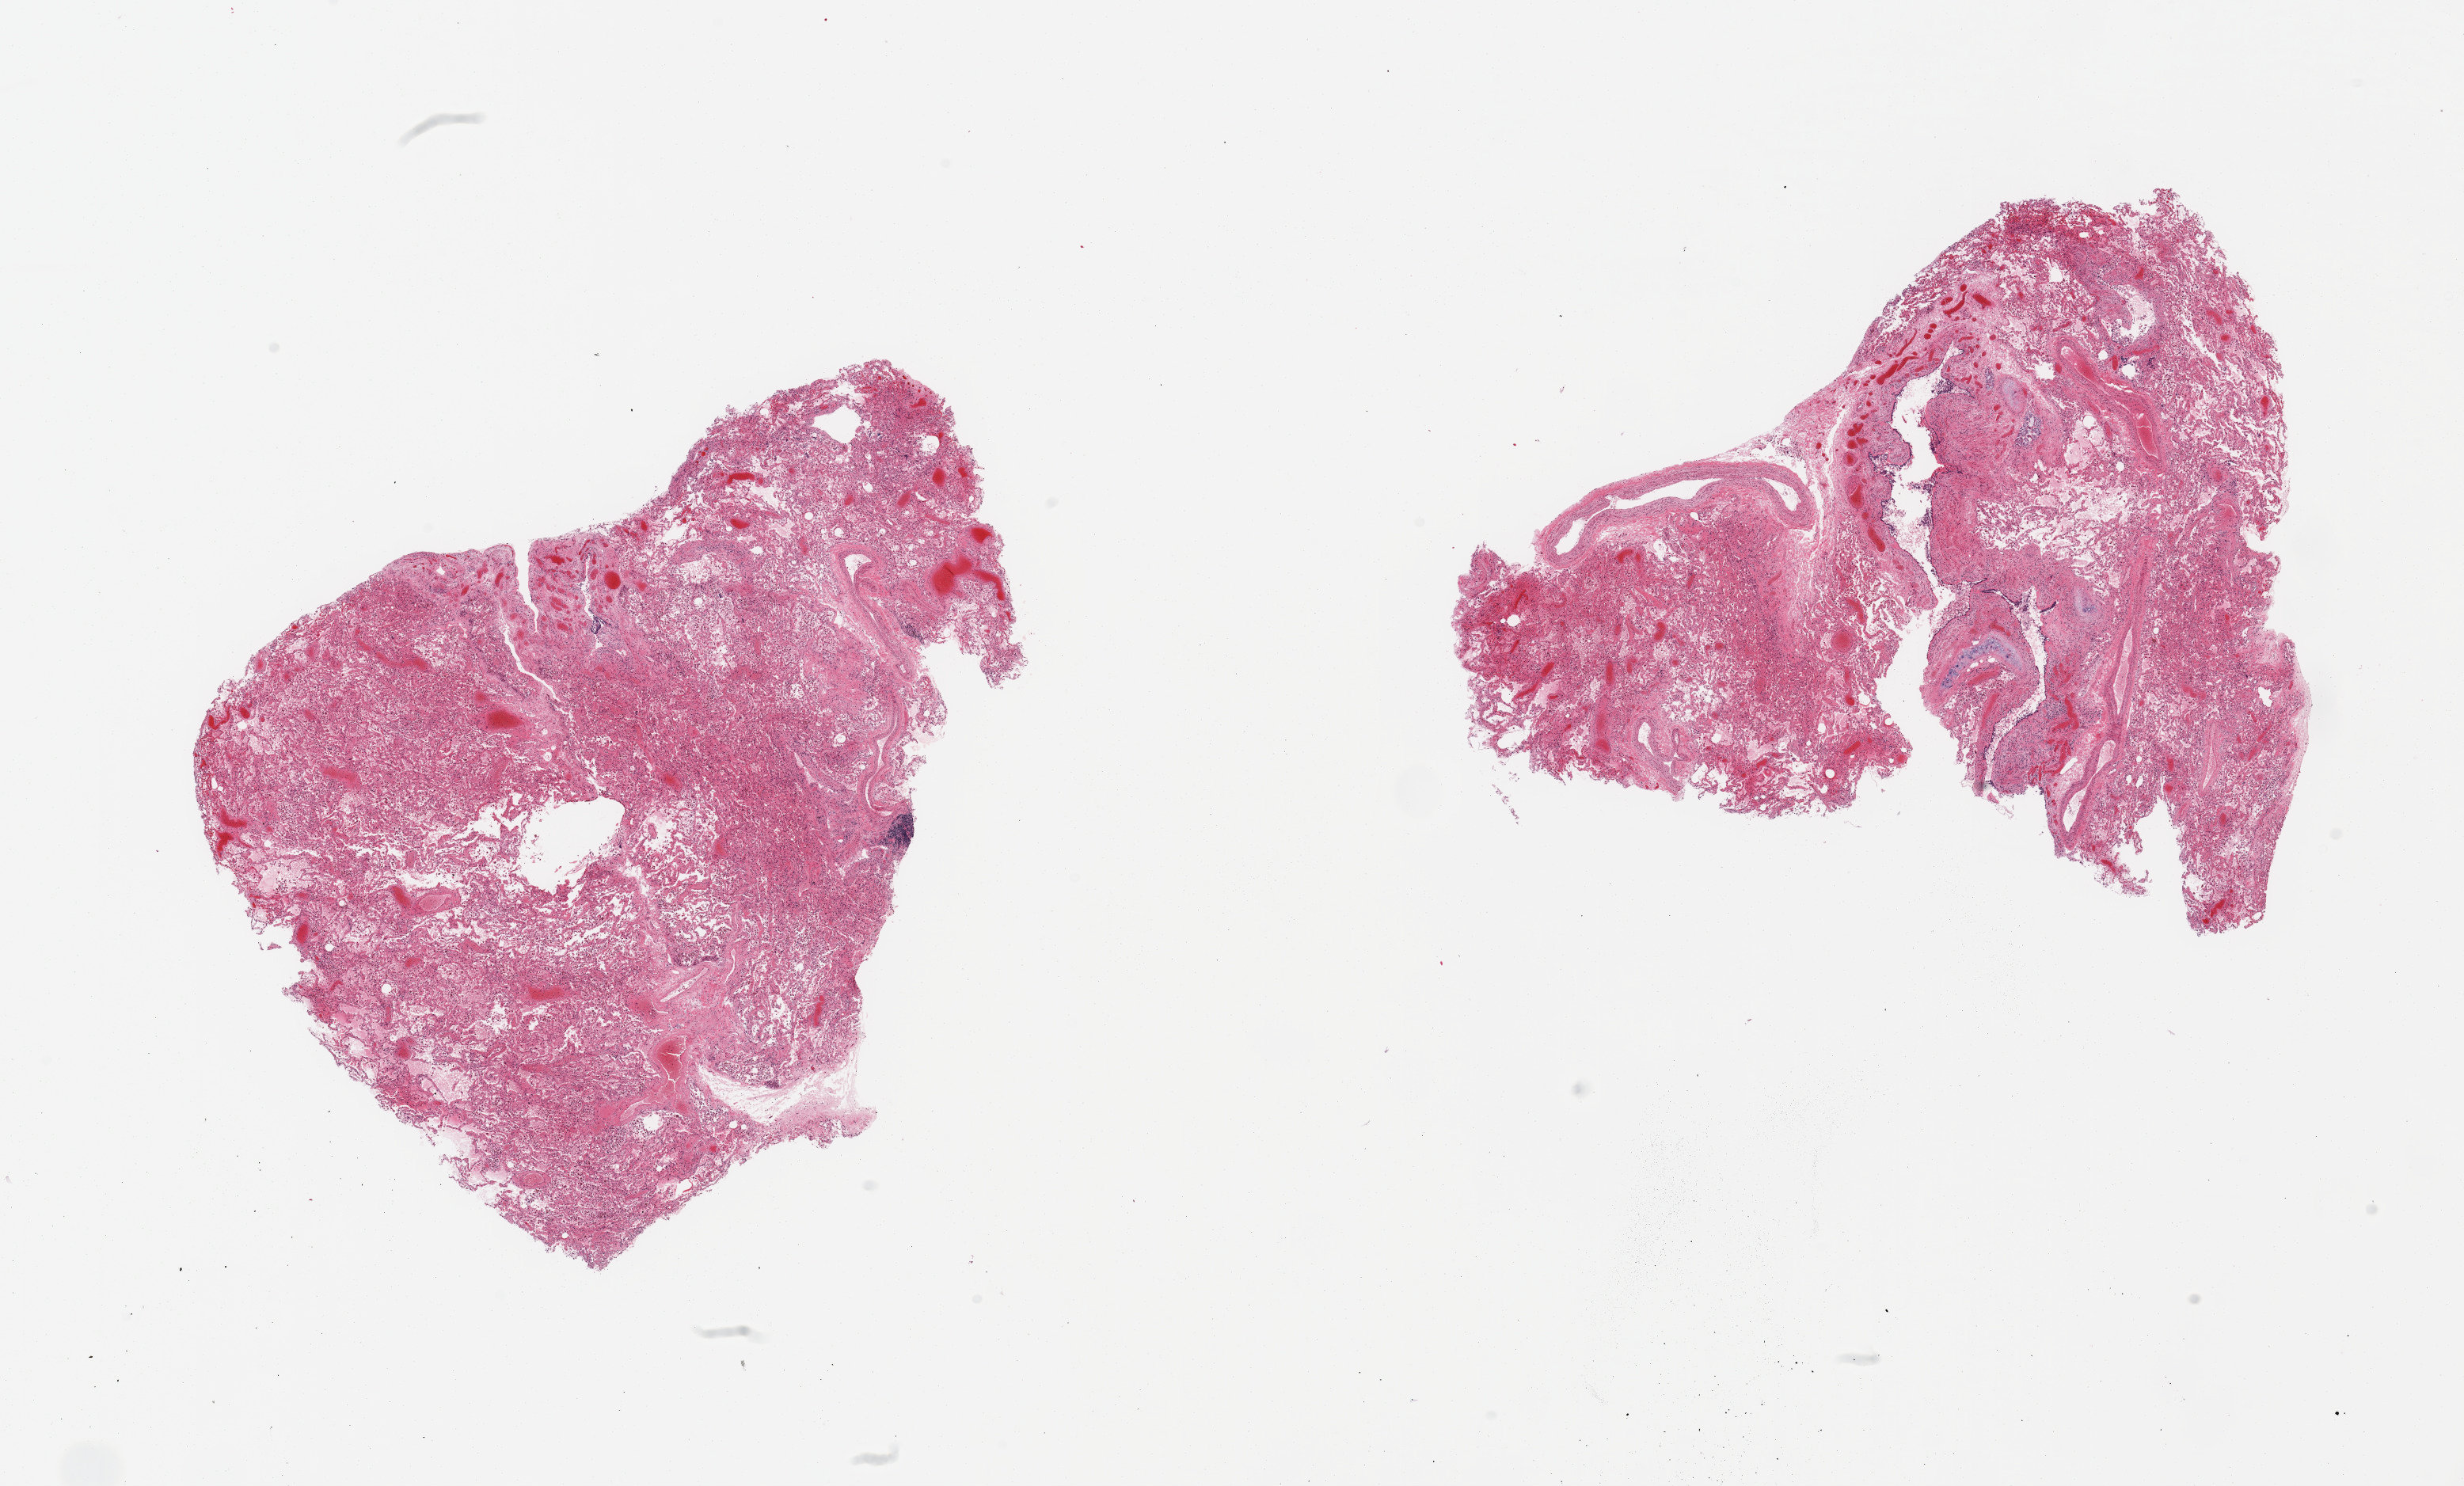
Whole-slide image, hematoxylin and eosin (H&E) stain — whole scanned area (about 24.6 x 14.8 mm, acquisition: 20x scan) shown as a low-resolution overview, PAXgene-fixed paraffin-embedded (PFPE) section, sampled site (target tissue): lung, tissue donor sample.
Review note (as recorded): 2 pieces, moderate congestion/edema, atalectasis. Approaching score 2 in some areas.